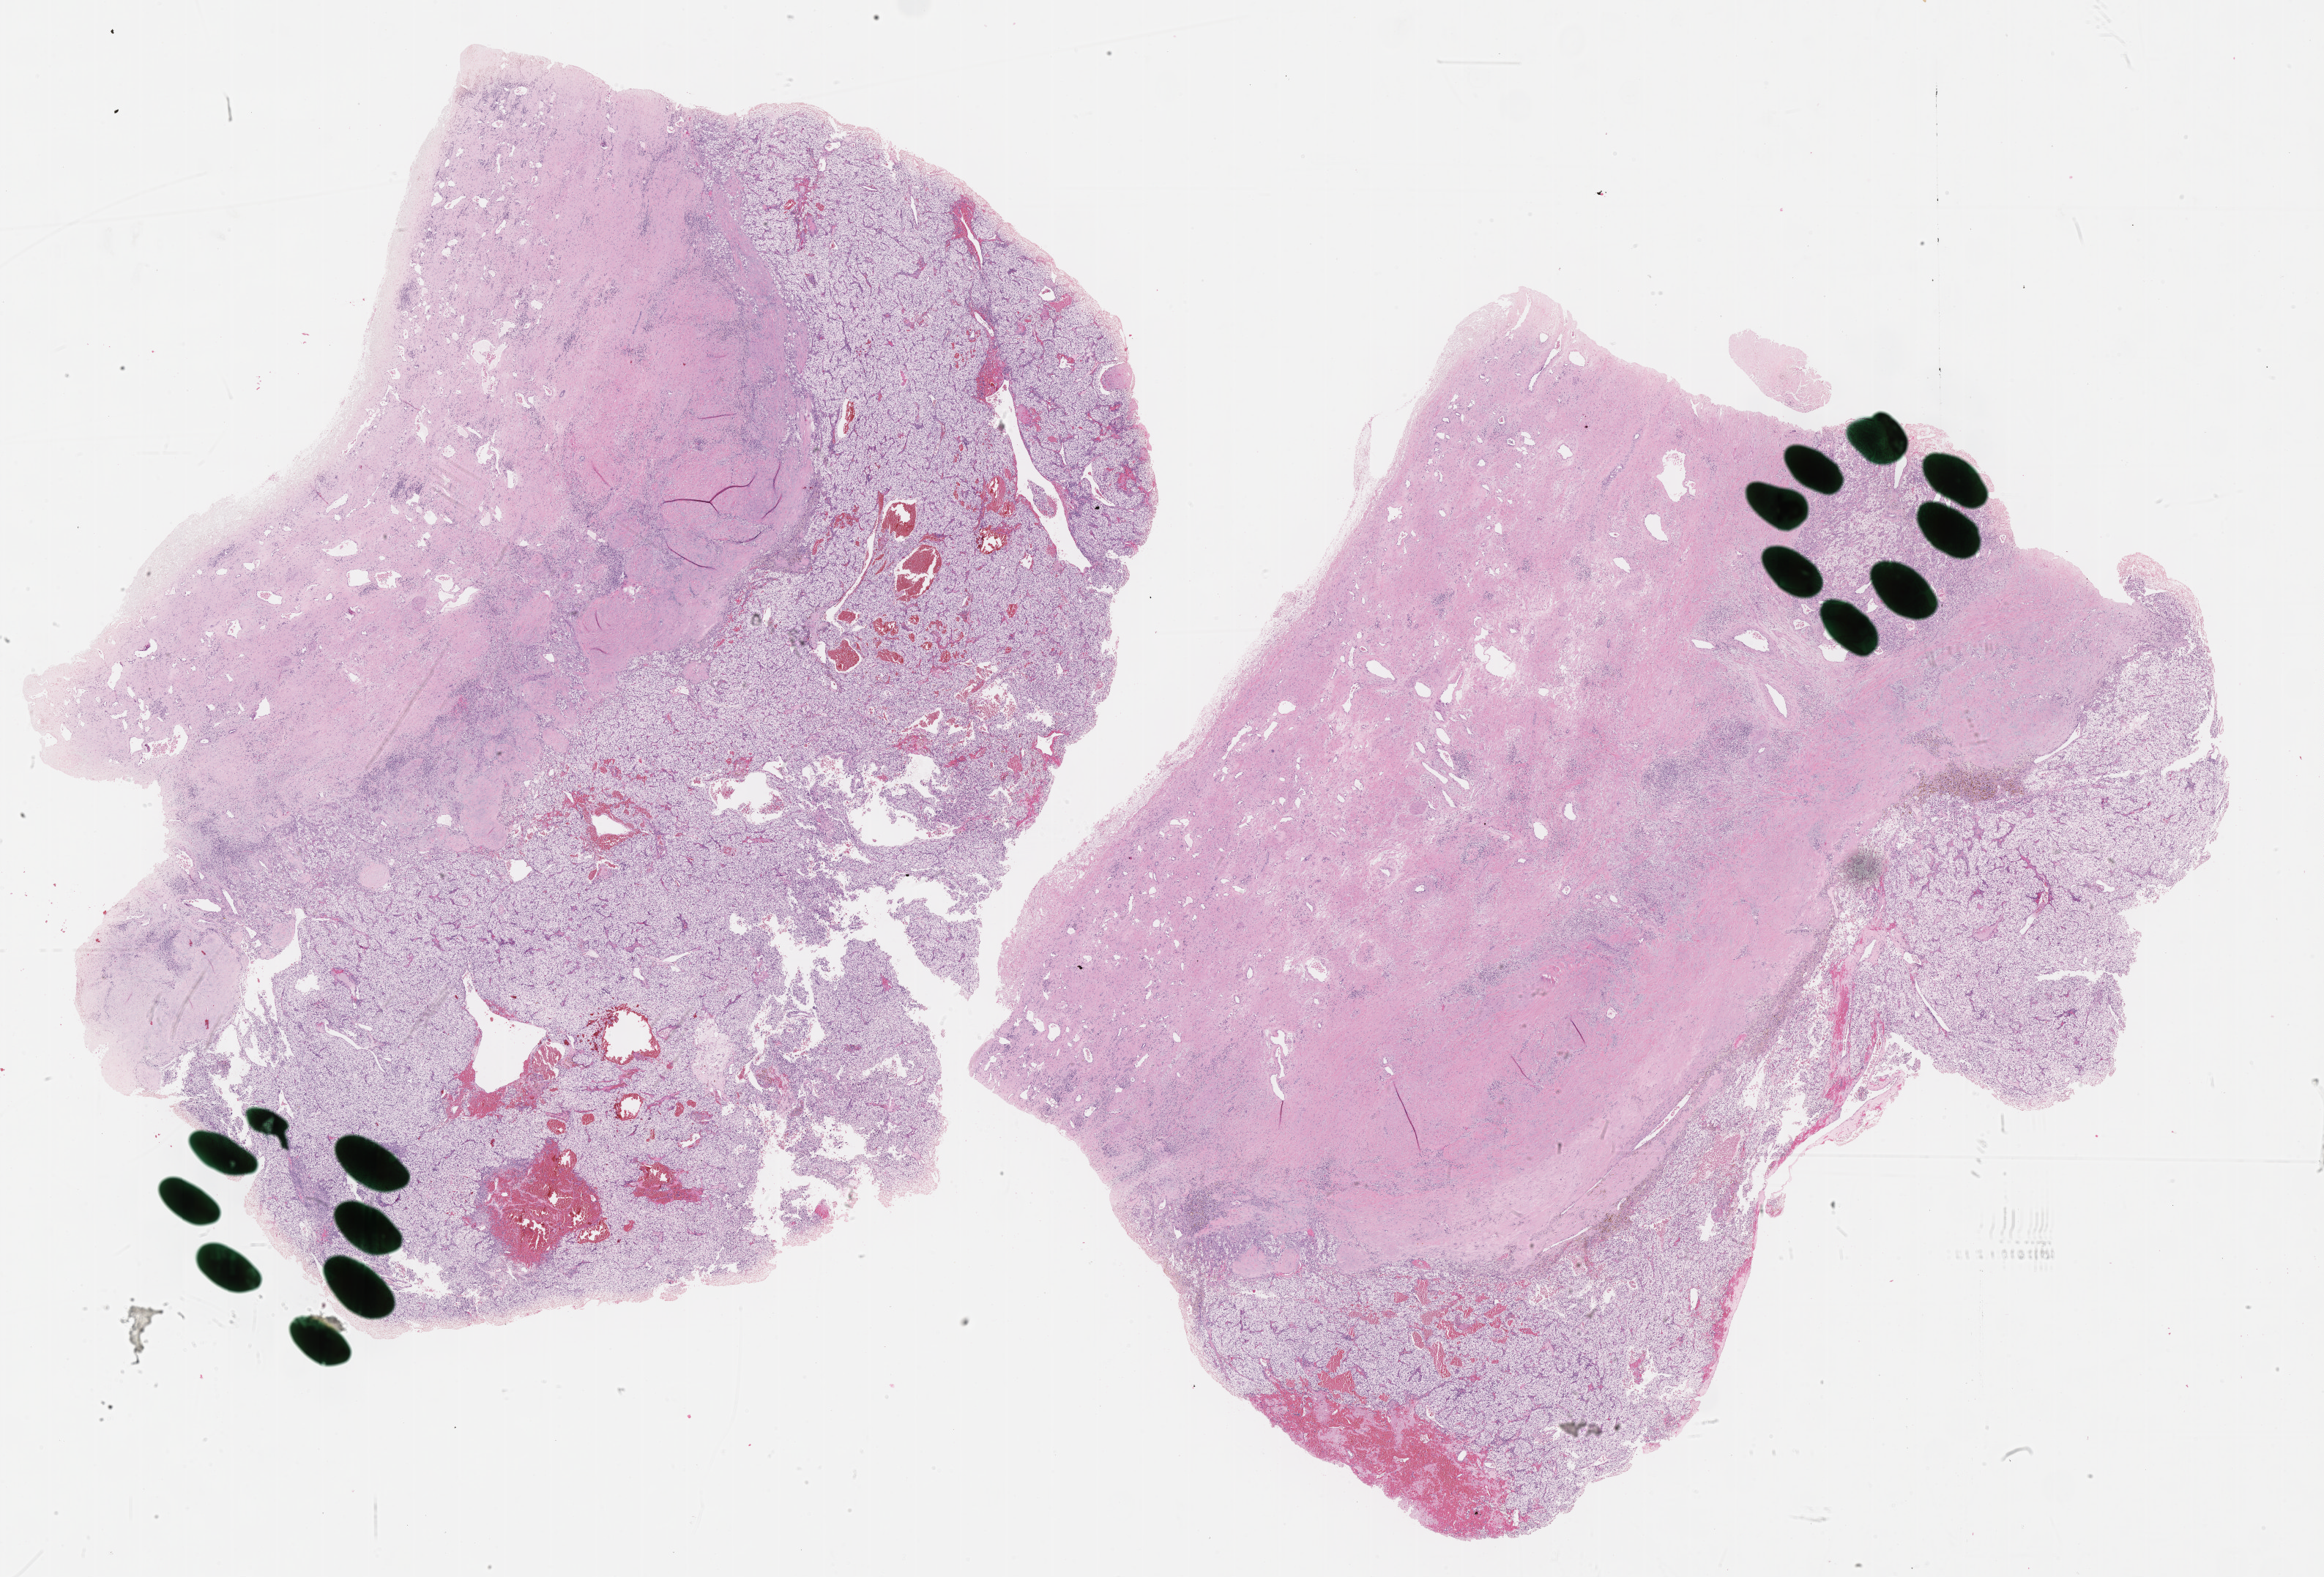
Whole-slide histology image, Hematoxylin and eosin (H&E) stained — shown as a low-resolution overview of the whole scanned area (about 25.7 x 17.4 mm). Formalin-fixed paraffin-embedded (FFPE) diagnostic section. Primary tumour sample from the kidney. Patient: male, age at initial diagnosis 48 years. Histologic grade: G3 (poorly differentiated).
* pathologic diagnosis: Clear cell adenocarcinoma, NOS
* AJCC pathologic stage: I